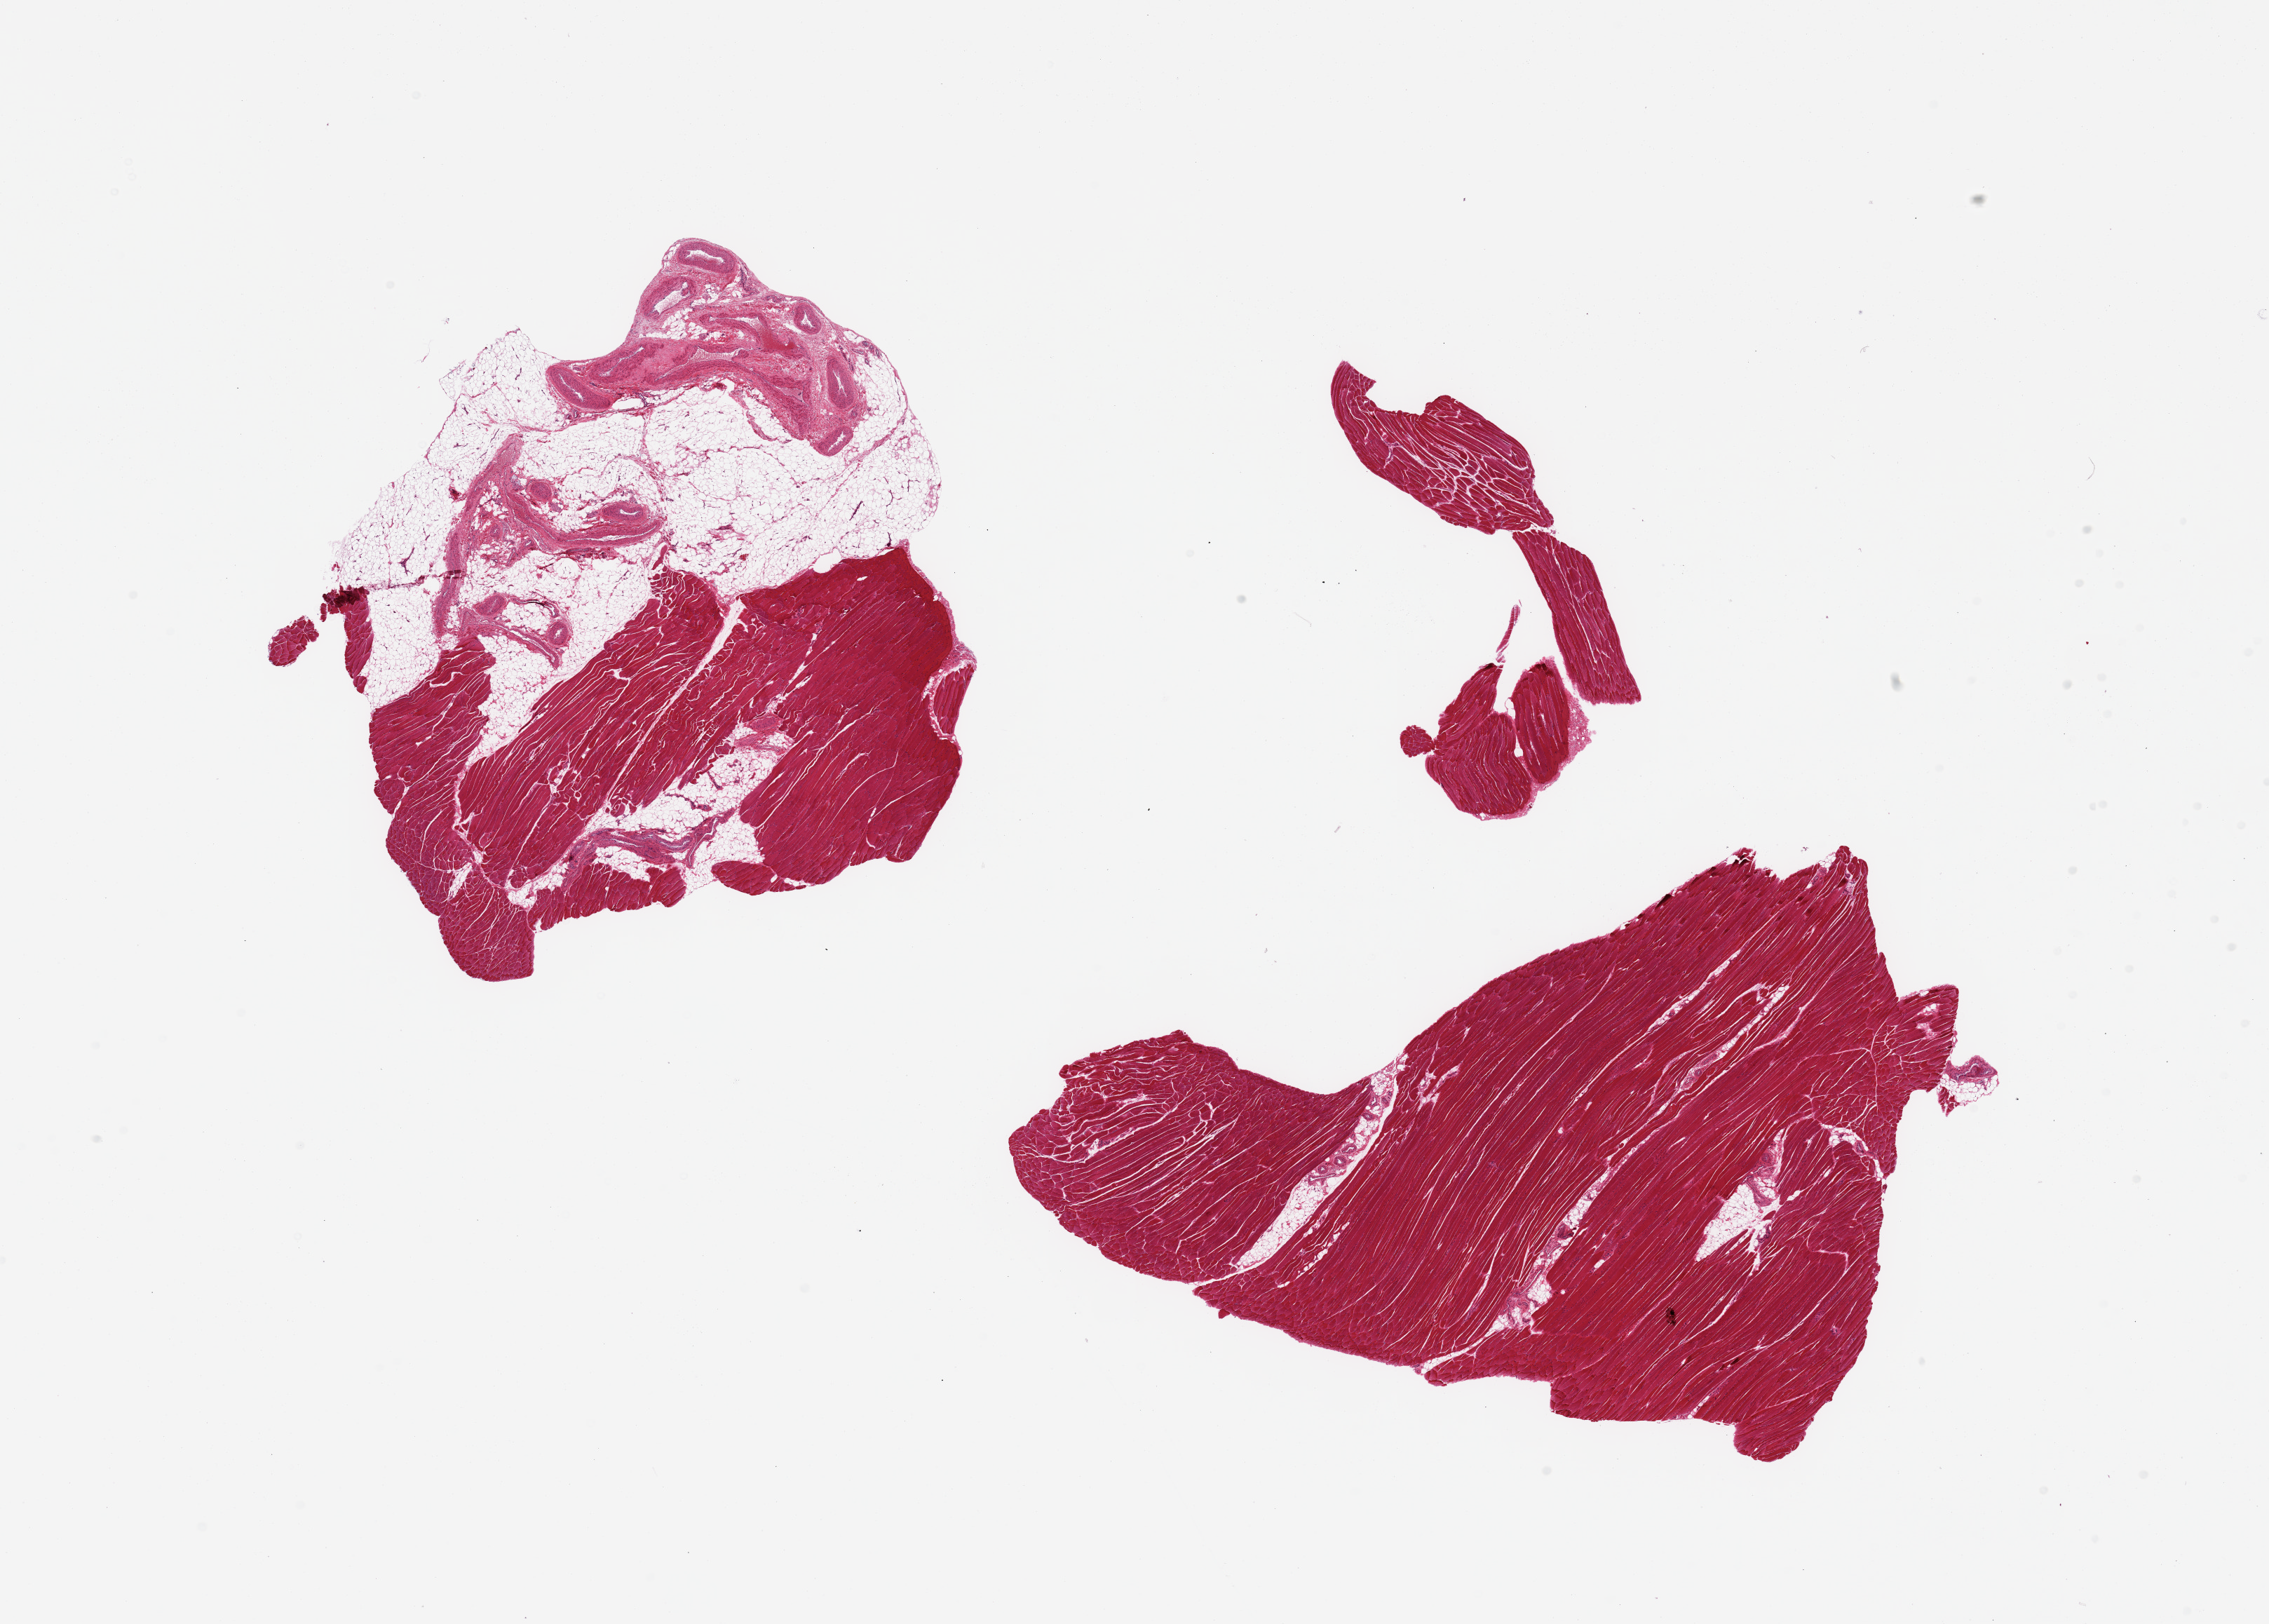
H&E whole-slide image — shown as a low-resolution overview of the whole scanned area (about 25.6 x 18.3 mm), PAXgene-fixed, paraffin-embedded tissue, target tissue: skeletal muscle, tissue donor sample. Donor: female.
• review note (as recorded): 2 pieces, ~30% adherent/interstitial fat/vascular elements; Sample carefully